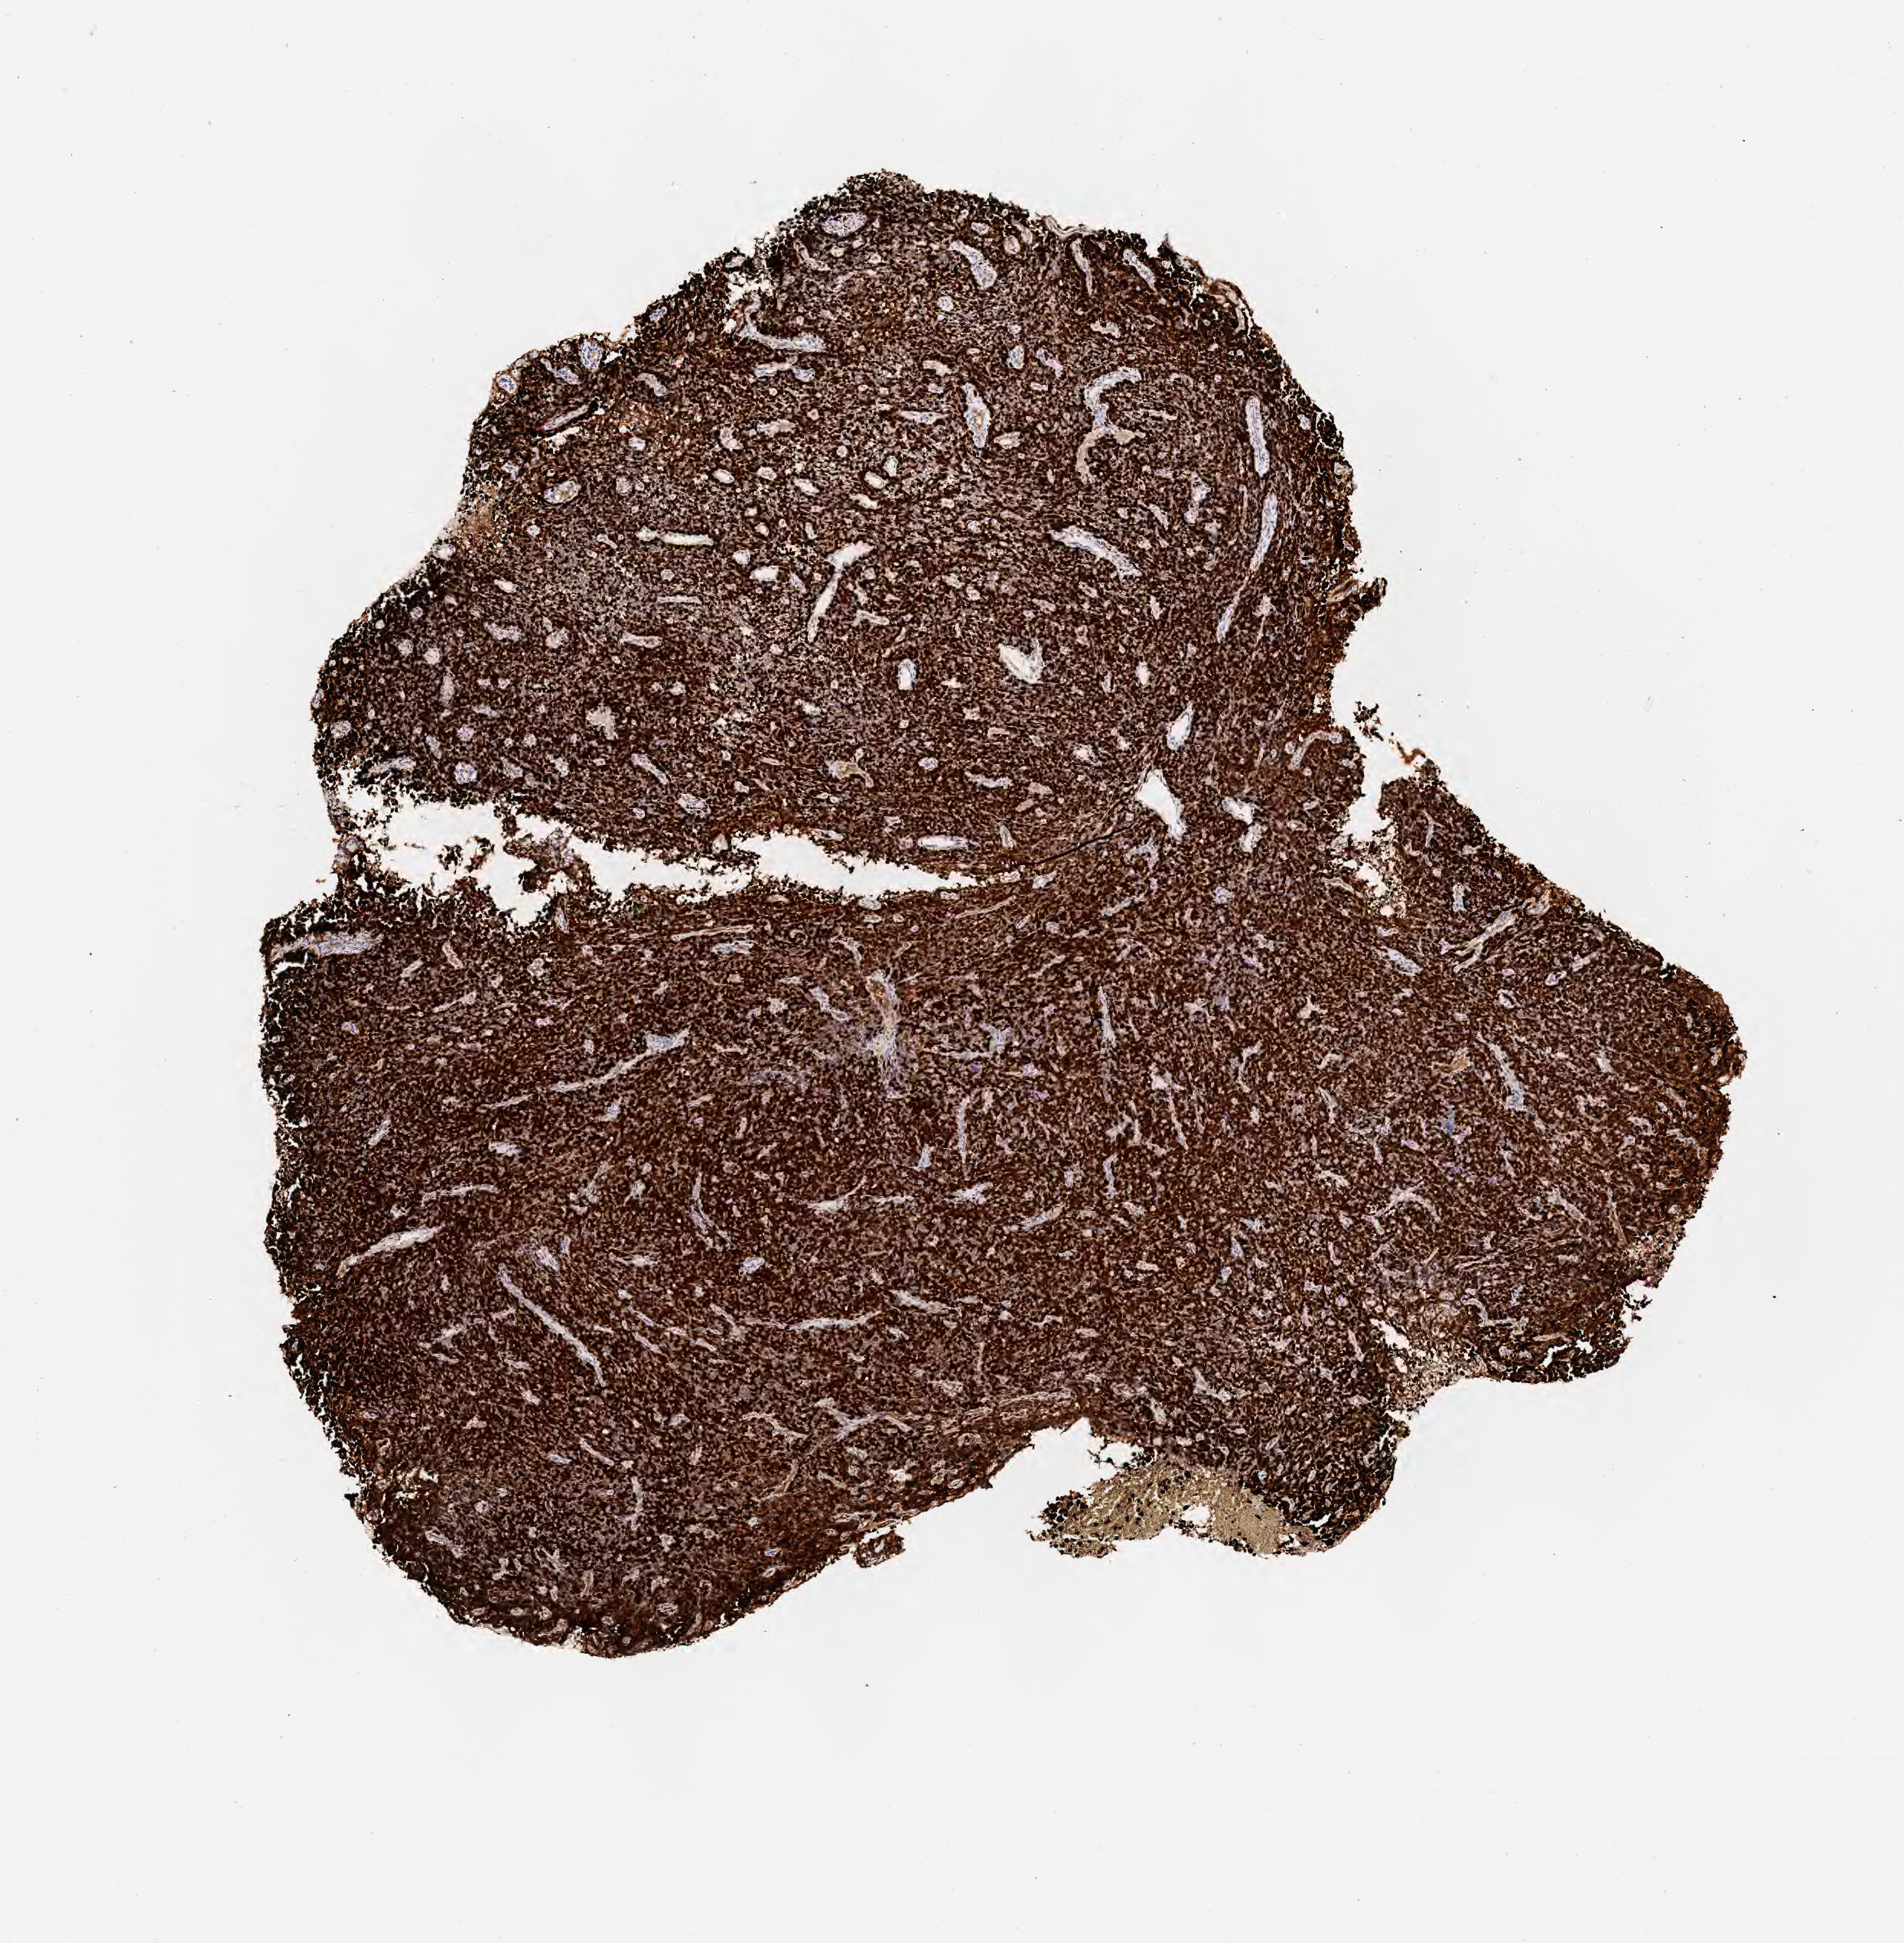
Whole-slide image, immunohistochemical stain for p16 (p16INK4a) — whole scanned area (about 5.0 x 5.1 mm) shown as a low-resolution overview. Specimen: tumor tissue. Site: cervix. Female patient, 70 years old.
• histologic diagnosis: Squamous cell carcinoma, large cell, nonkeratinizing, NOS